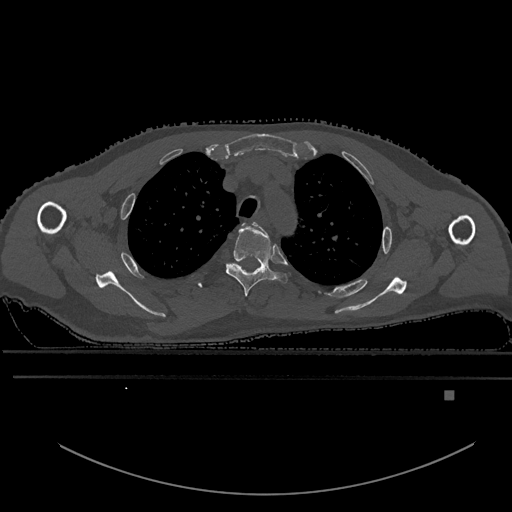
CT including the spine, one axial slice. Position 450 of 969 along the scan axis. Bone window (W 1800 / L 400 HU). 512 × 512 image matrix. Male patient, age 82 years. From the clinical record (not read from this slice): primary cancer: prostate.
Structures marked on this image (semi-automatically segmented with operator editing):
- T2 vertebra: bounding box <242,223,259,226> (left, top, right, bottom; pixels)
- T3 vertebra: <225,222,288,297>
- T4 vertebra: <228,263,237,266>